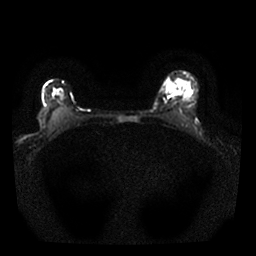
Breast MRI, one axial slice. Position 18 of 25 along the scan axis. Diffusion-weighted series; image 2 of 4 stored at this slice position (different b-values; order by instance number). 1.5 T. 4 mm slice thickness. 256 × 256 image matrix, field of view 310 × 310 mm. Female patient.
Outlined on this slice (manually delineated by an expert):
- tumour on diffusion-weighted imaging: box from (x=166, y=83) to (x=177, y=94) px